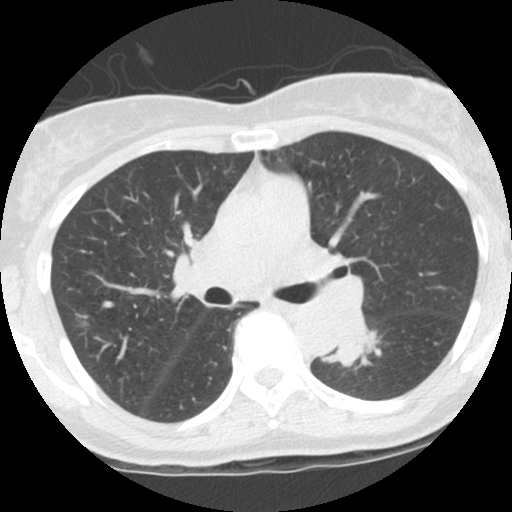
Low-dose screening chest CT, one axial slice. Position 67 of 115 along the scan axis. 120 kVp. Lung window (W 1500 / L -600 HU). 2.5 mm slice thickness. 512 × 512 image matrix.
Annotated regions visible in this slice (manually delineated by an expert):
- lesion 1 (tumor, lower lobe of left lung): bounding box (x1, y1, x2, y2) in pixels: (323, 324, 370, 366)